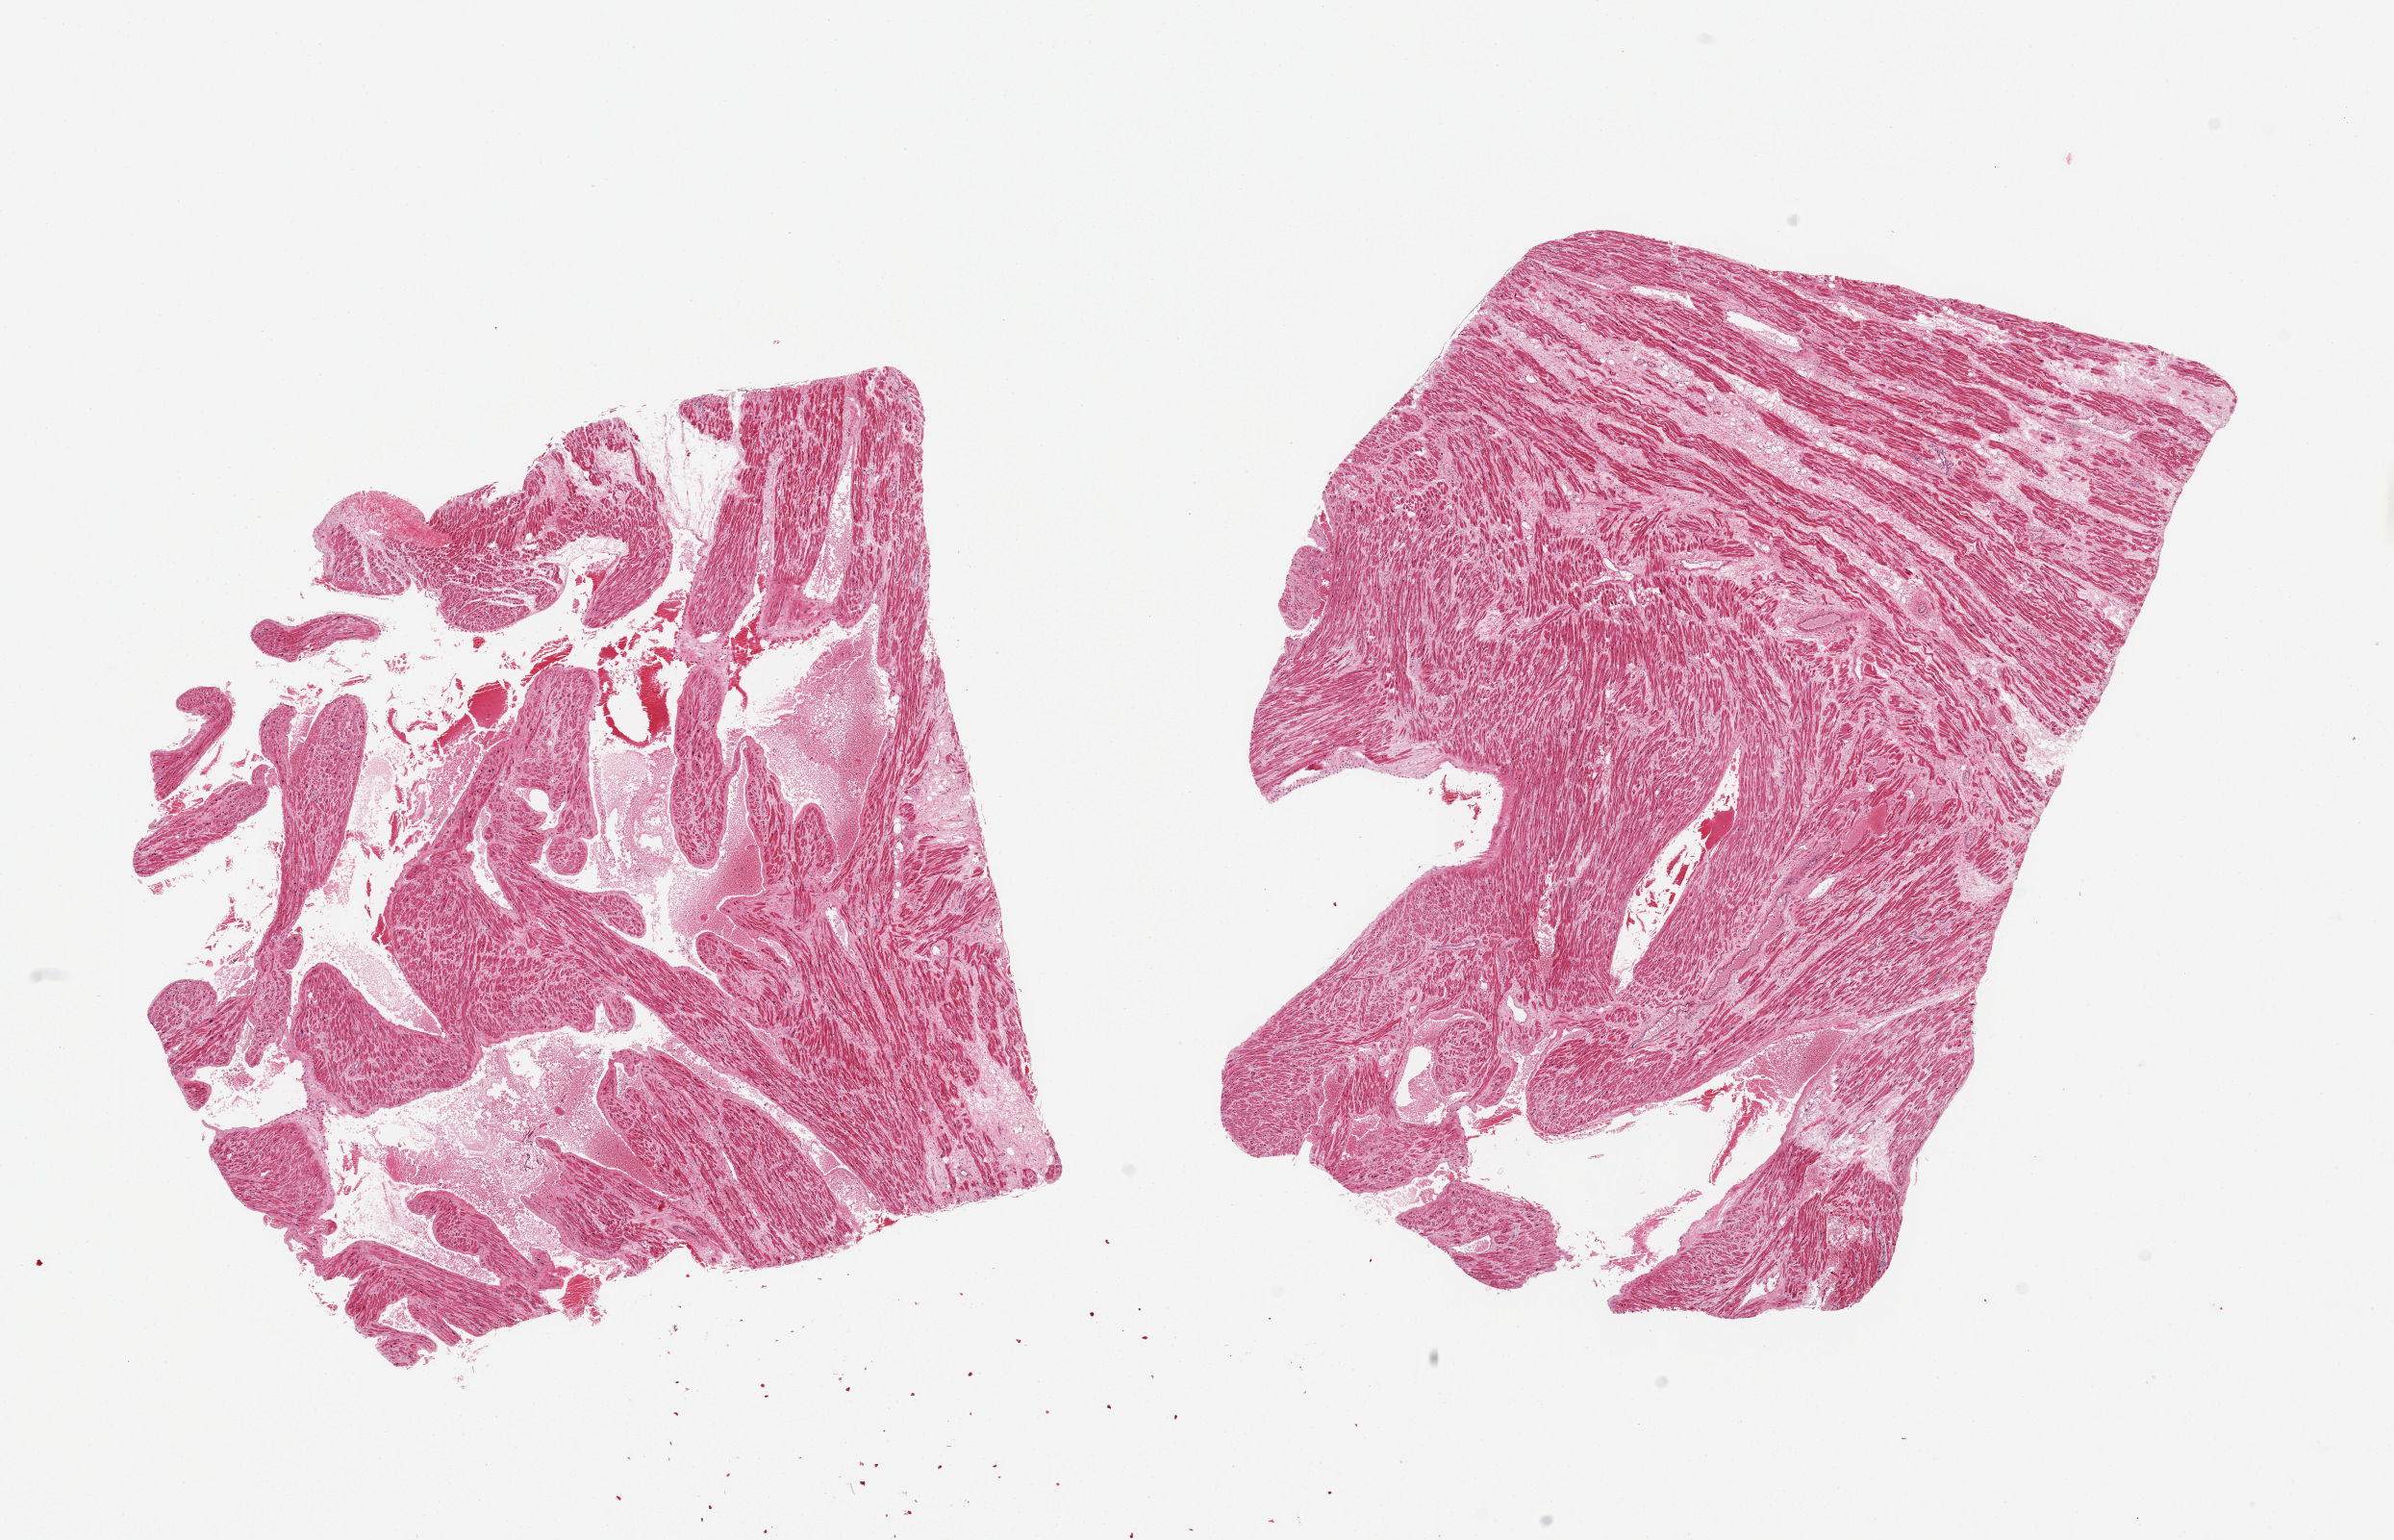
Digitized H&E-stained section, brightfield — whole scanned area (about 19.7 x 12.7 mm, from a 20x scan) shown as a low-resolution overview; PAXgene-fixed, paraffin-embedded tissue; target tissue: auricular appendage; donor tissue sample. Donor sex: male.
• review note (as recorded): 2 pieces; minimal fat